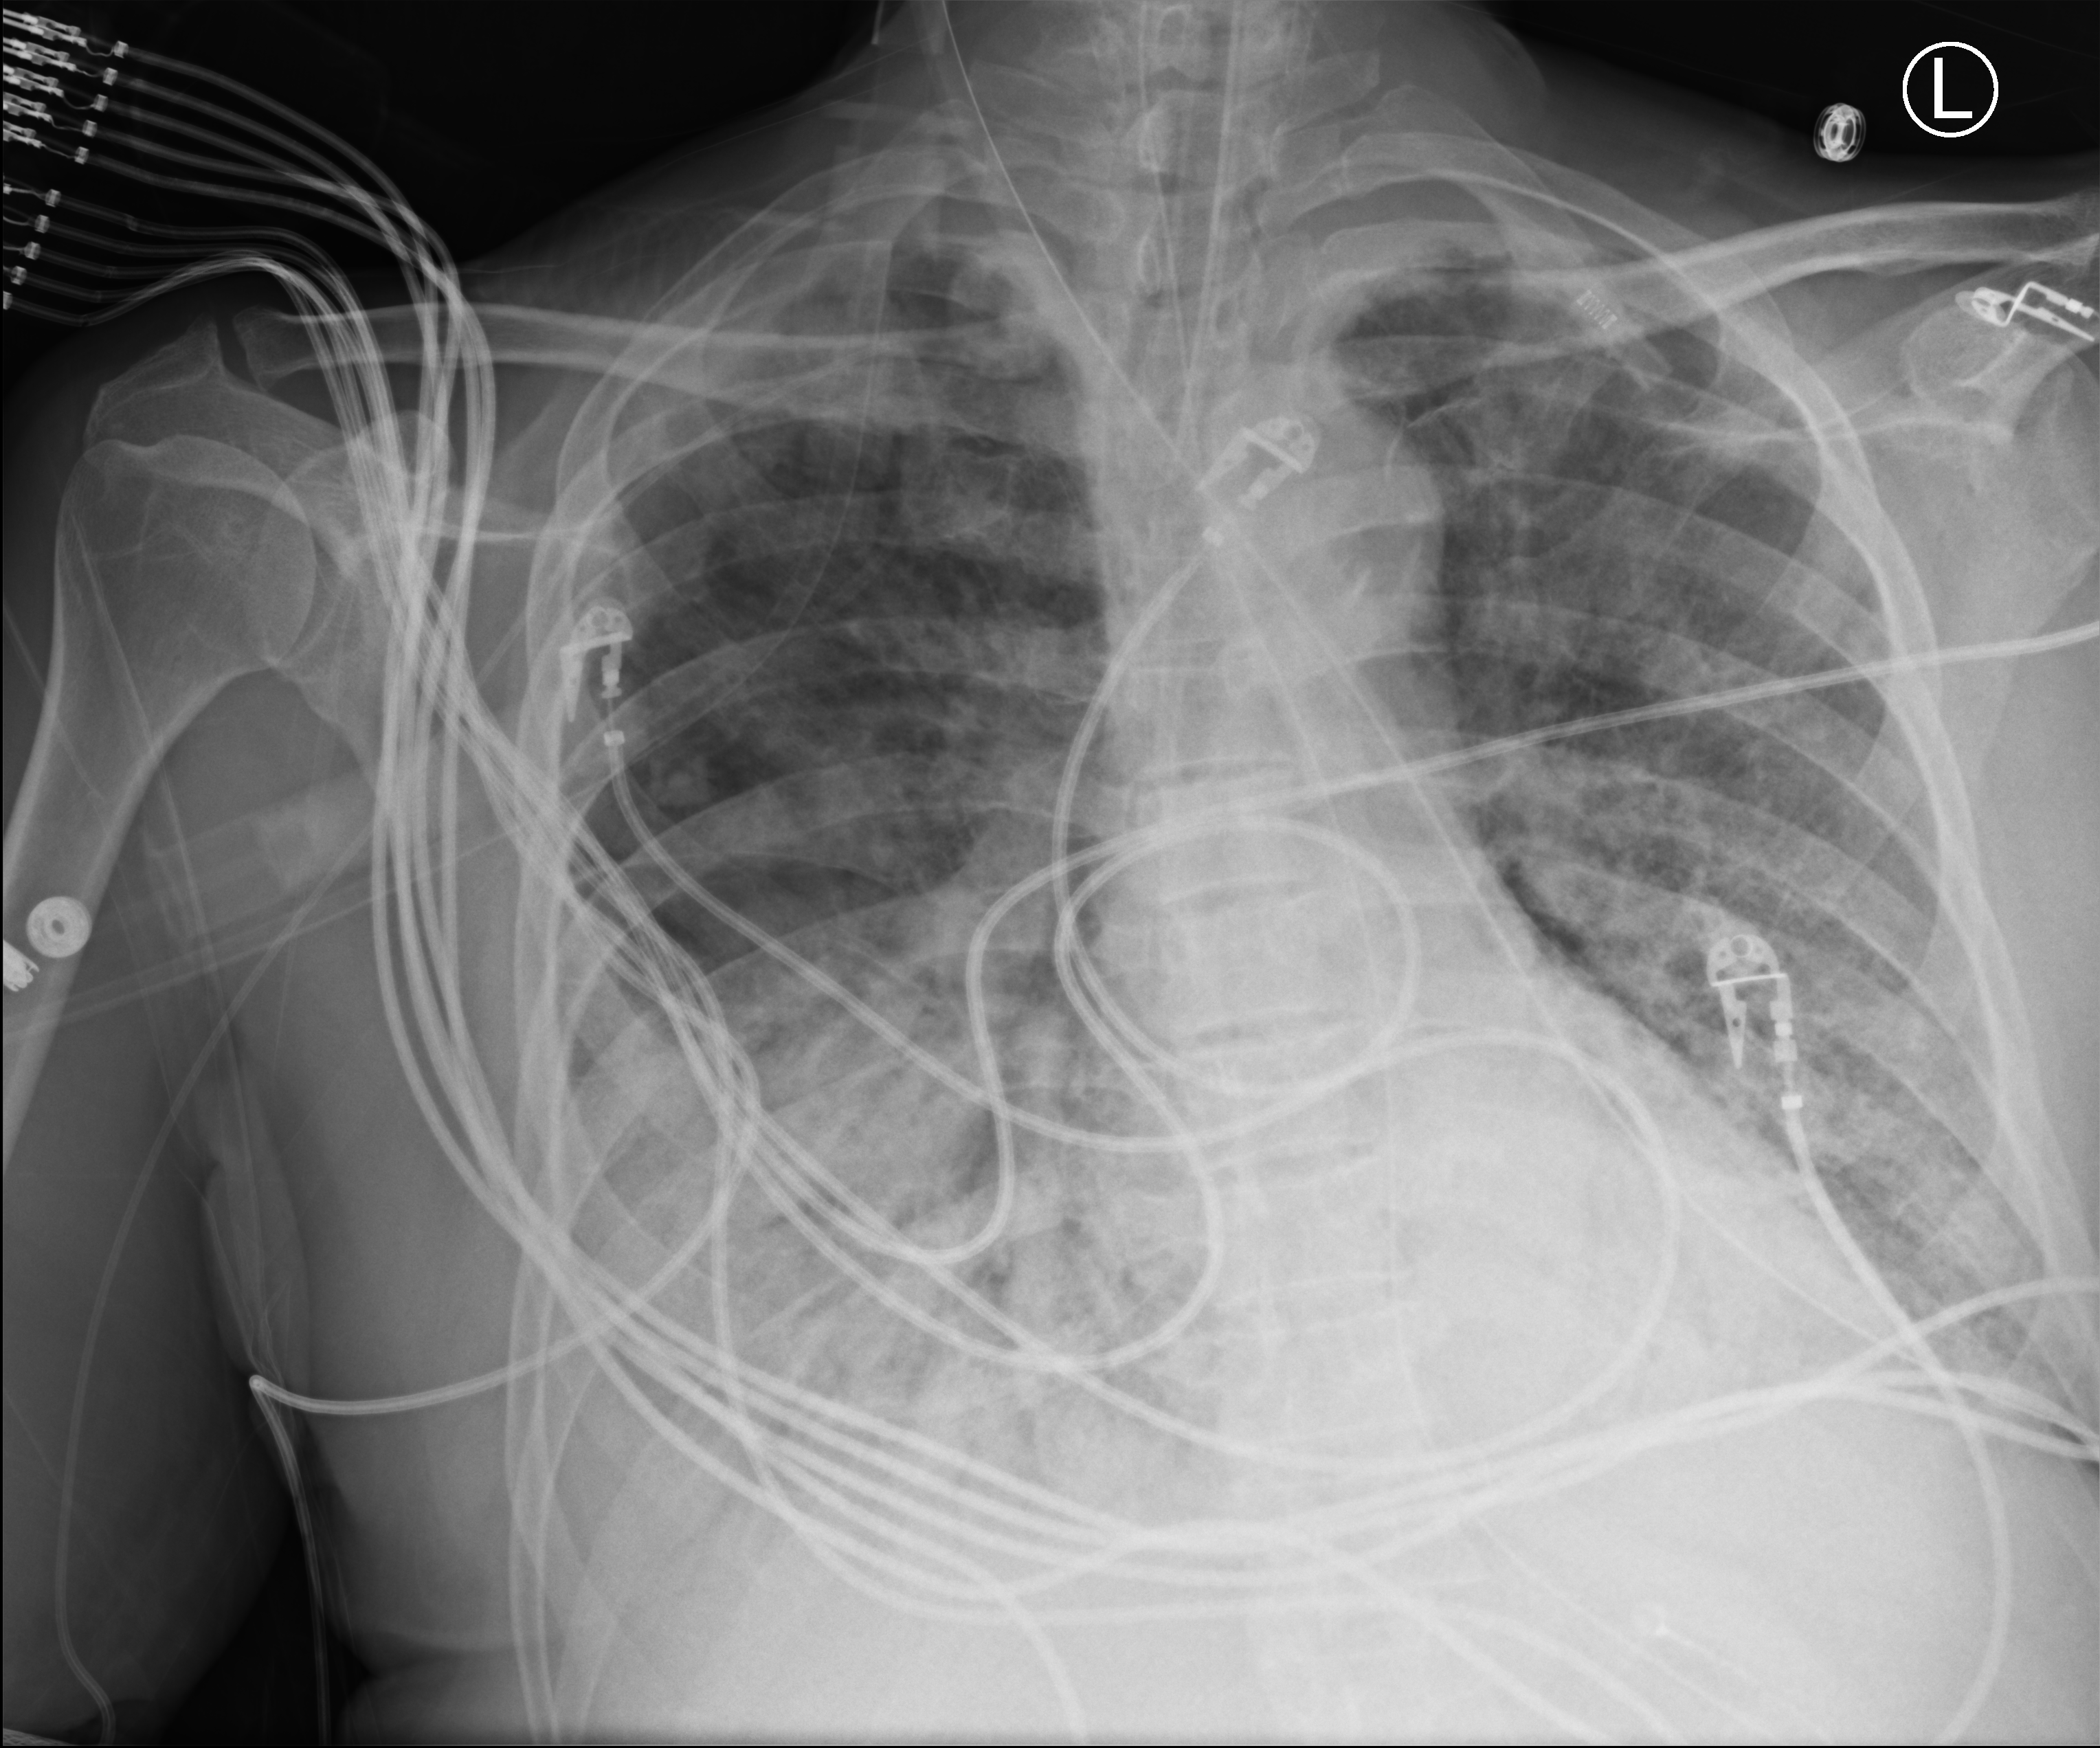
Portable chest radiograph; anteroposterior (AP) projection. Patient hospitalised with COVID-19; male, aged 60–74 years.
From the hospital-stay record, not from the radiograph (when in the stay this image was taken is not recorded):
- length of hospital stay: 31 days
- admitted to intensive care during this hospital stay: yes